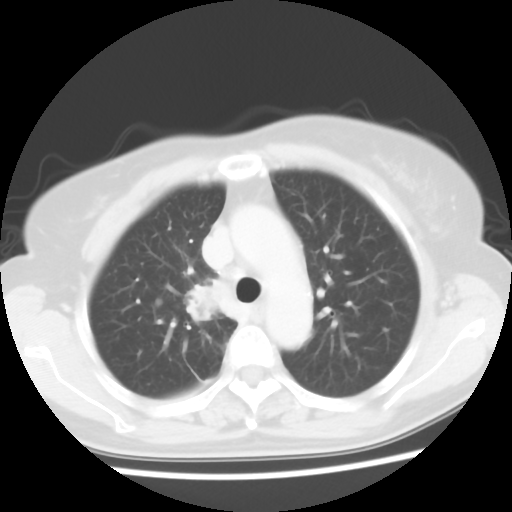
Chest CT, one axial slice. Slice 41 of 56 in the series (ordered by position). Reconstruction kernel STANDARD. Lung window (W 1500 / L -600 HU). 5 mm slice thickness. 512 × 512 image matrix, field of view 314 × 314 mm. Female patient, age 62 years. From the clinical record (not read from this slice): clinical TNM (as recorded): T2 N1 M1a.
Outlined on this slice (bounding box drawn by a radiologist):
- lung tumour (recorded histology: adenocarcinoma): bounding box <178,267,231,321> (left, top, right, bottom; pixels)